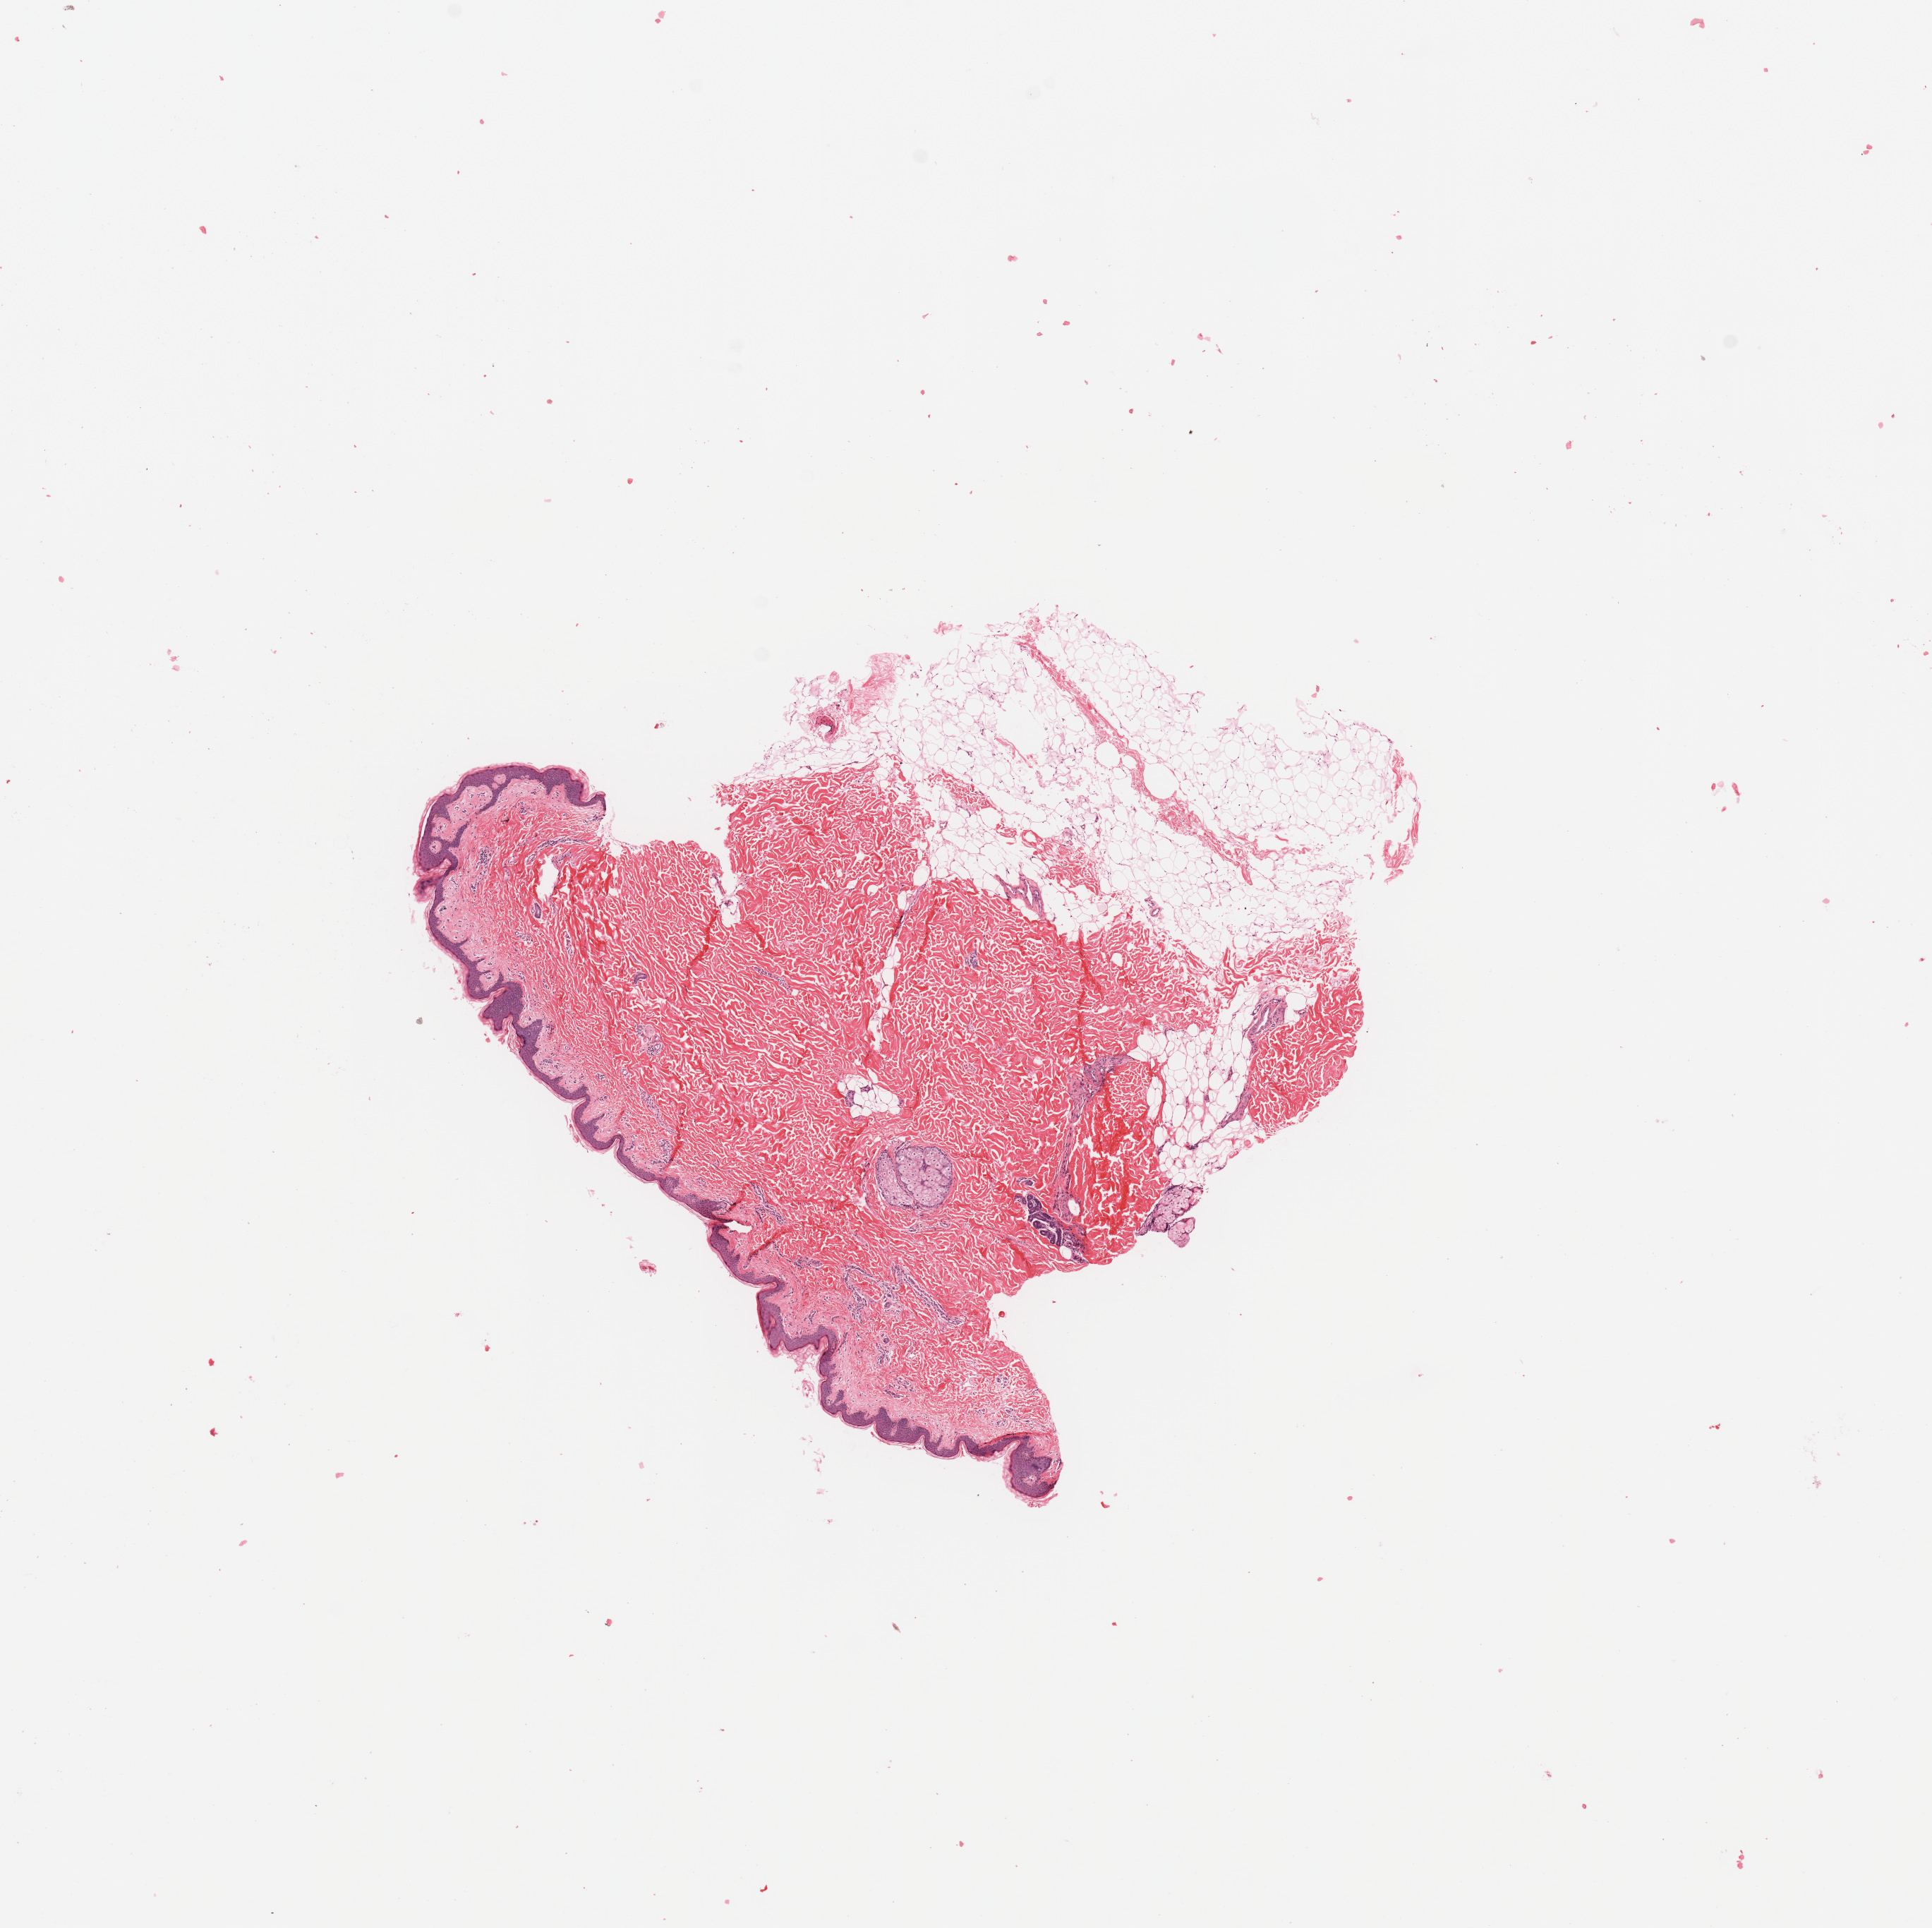
Digitized H&E-stained tissue section (whole slide), low-resolution overview of the scanned area, about 10.8 x 10.8 mm. Normal (non-tumour) tissue (melanoma cohort); sampled site not recorded. Patient: female, age 49 years.
This section: normal (non-tumour) tissue from the same patient. Patient diagnosis: Malignant melanoma, NOS.